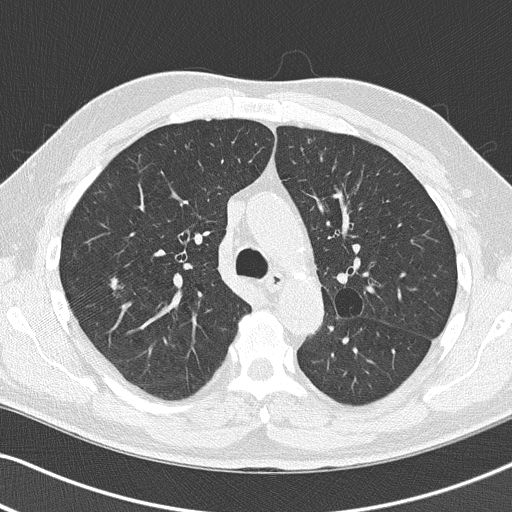
Low-dose screening chest CT, one axial slice. Slice 91 of 140 in the series (ordered by position). Reconstruction kernel B50f. Lung window (W 1500 / L -600 HU). 512 × 512 image matrix, field of view 330 × 330 mm.
Annotated regions visible in this slice (outlined manually by an expert reader):
- lesion 1 (tumor, upper lobe of right lung): box from (x=111, y=279) to (x=119, y=288) px